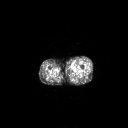
FDG PET of an extremity soft-tissue mass (from a PET/CT study), one axial slice. Slice 235 of 267 in the series (ordered by position). 3.27 mm slice thickness. 128 × 128 image matrix, field of view 700 × 700 mm. Male patient, age 48 years. From the clinical record (not read from this slice): histological type: pleiomorphic leiomyosarcoma; grade: high; site of the primary tumour: left thigh.
Structures marked on this image (expert contour drawn on MRI and transferred to this co-registered scan by the dataset authors):
- gross tumour volume including surrounding oedema: box from (x=70, y=65) to (x=74, y=69) px